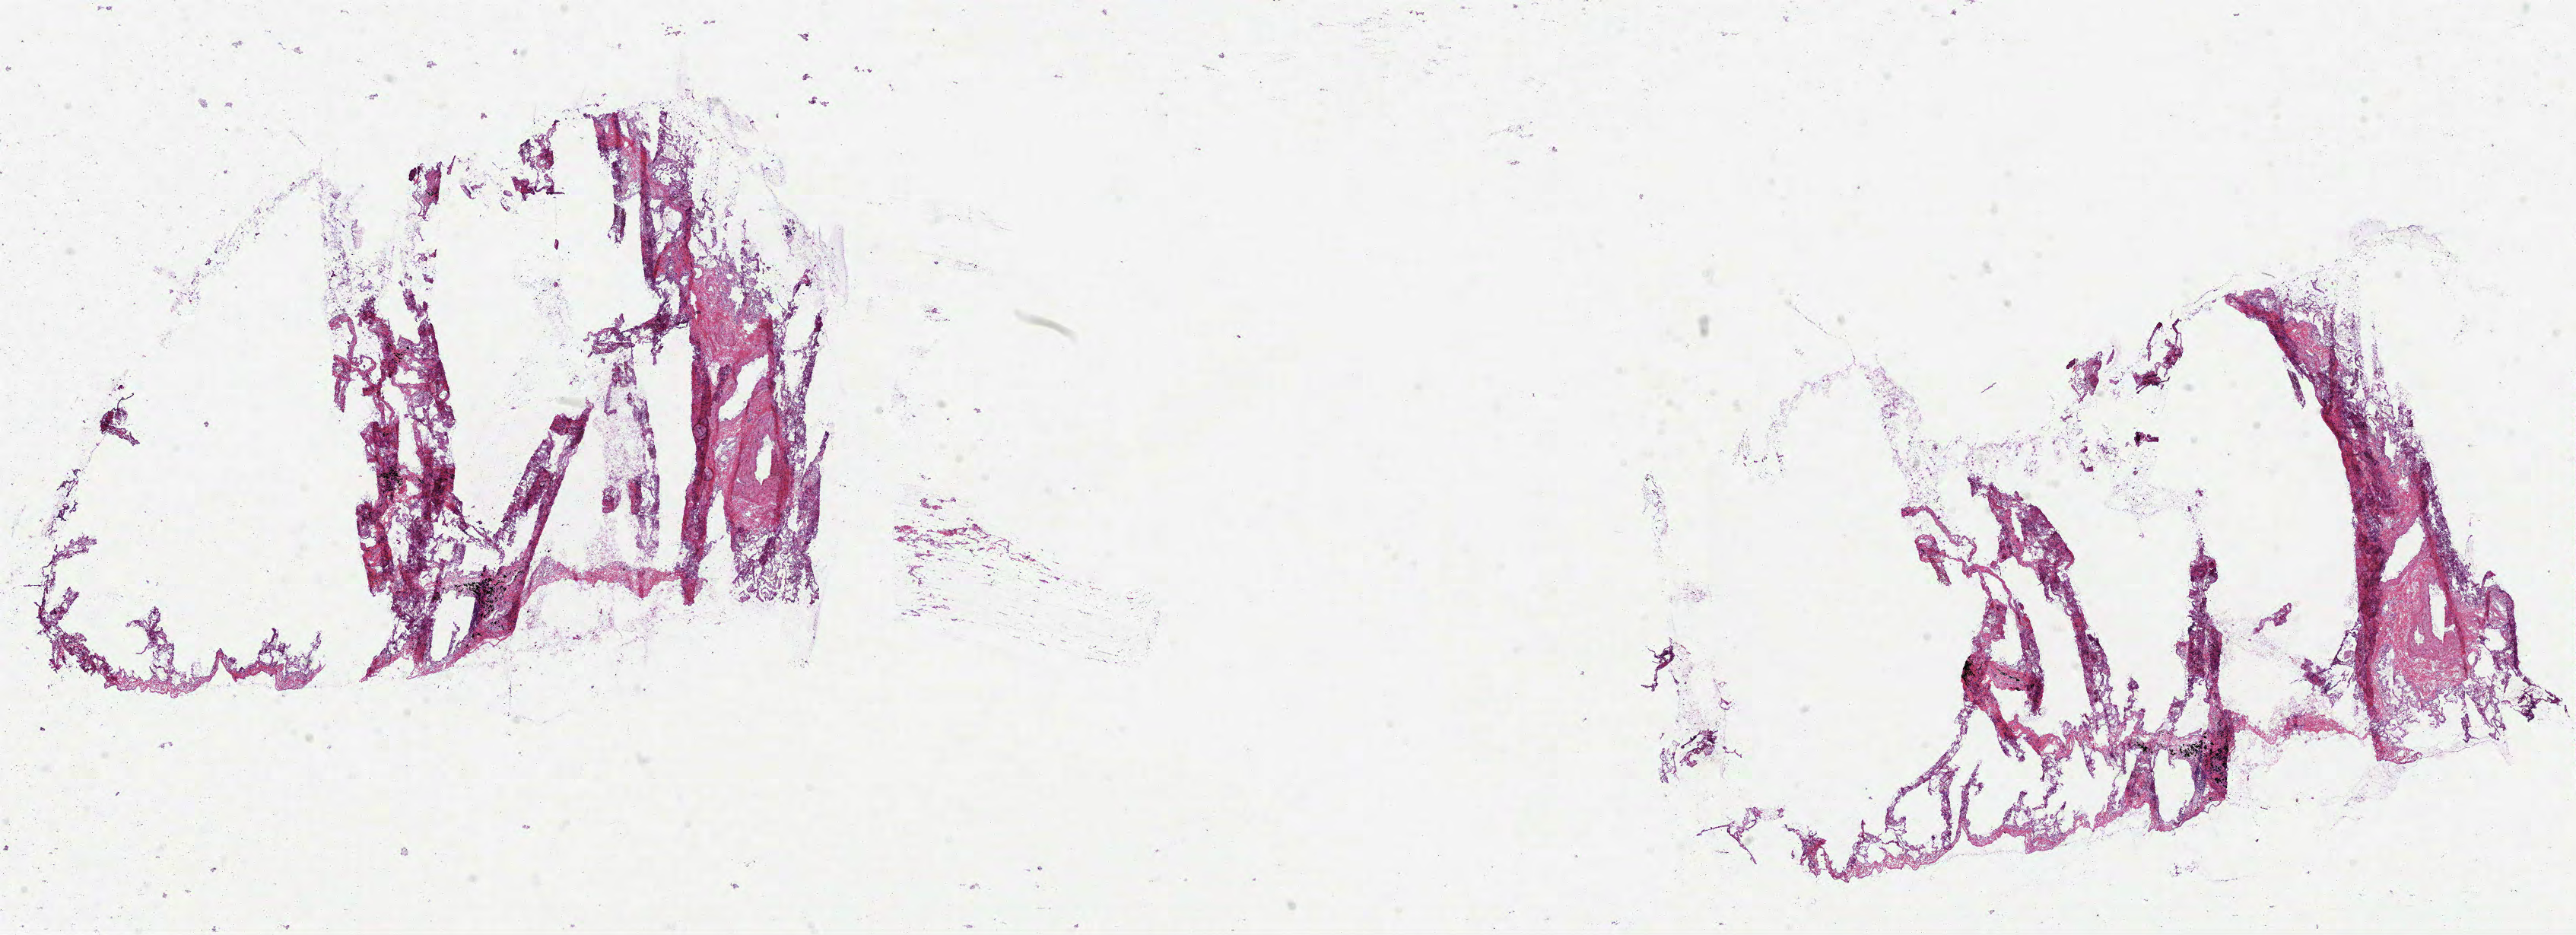
H&E-stained whole-slide image — a low-resolution overview of the entire scanned area, about 27.3 x 9.9 mm. Frozen section from the top of the tissue portion. Lung, solid tissue normal (non-tumour tissue) sample. Female, age 72 years at initial diagnosis. Inflammatory infiltration, as recorded: lymphocyte infiltration 2%, monocyte infiltration 5%, neutrophil infiltration 1%.
This section: solid tissue normal (non-tumour) sample from the same patient. Patient diagnosis: Squamous cell carcinoma, NOS (lower lobe, lung).